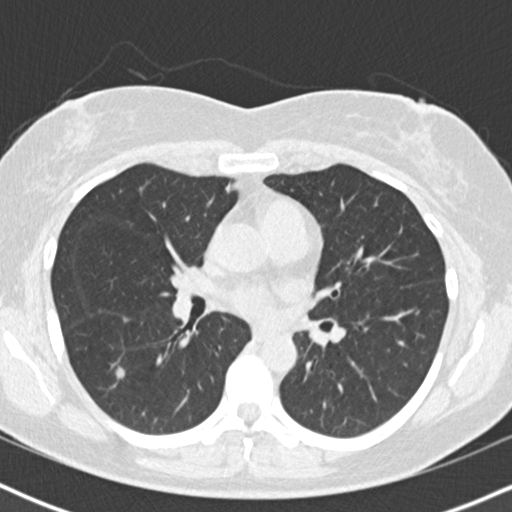
Low-dose screening chest CT, one axial slice; slice 92 of 167 in the series (ordered by position); reconstruction kernel B30f; 120 kVp; lung window (W 1500 / L -600 HU); 2 mm slice thickness; 512 × 512 image matrix, field of view 320 × 320 mm.
Annotated regions visible in this slice (manually delineated by an expert):
- lesion 1 (tumor, lower lobe of right lung): bounding box (x1, y1, x2, y2) in pixels: (116, 367, 125, 379)